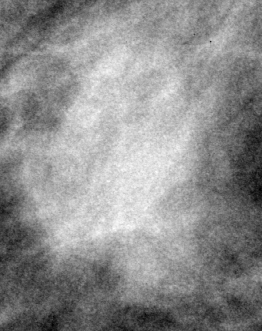
Region of interest cut from a scanned film mammogram (one marked finding); right breast; MLO view; BI-RADS breast density category 2 (scale 1–4).
Finding: mass, shape irregular, margins spiculated; BI-RADS assessment category 5; subtlety rating 4 on a 1 (subtle) to 5 (obvious) scale; pathology (as recorded): malignant.